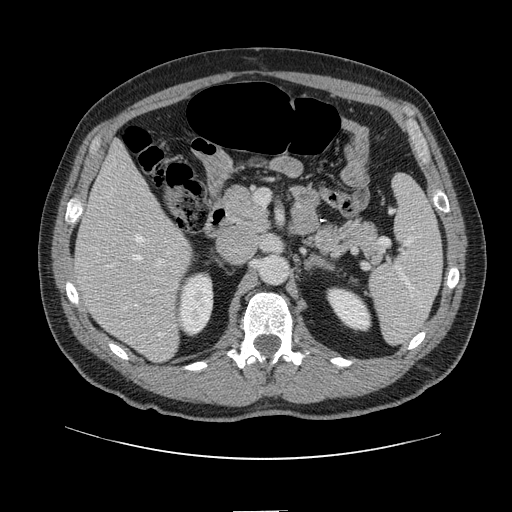
Contrast-enhanced abdominal CT, one axial slice; slice 61 of 161 in the series (ordered by position); 120 kVp; intravenous contrast given; soft-tissue window (W 400 / L 40 HU); 2.5 mm slice thickness; 512 × 512 image matrix, field of view 412 × 412 mm. Male patient, age 66 years. Case-level facts recorded for this patient, not image findings: diagnosis: colorectal cancer liver metastases, imaged before liver resection.
Annotated regions visible in this slice (expert manual segmentation):
- hepatic veins: bounding box (x1, y1, x2, y2) in pixels: (125, 235, 162, 336)
- liver: (76, 144, 192, 361)
- planned liver remnant (the part of the liver to remain after resection): (75, 143, 173, 284)
- portal vein (with intrahepatic branches): (150, 258, 165, 294)